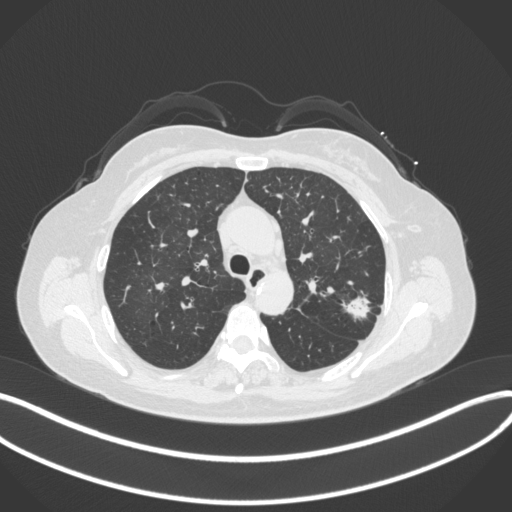
Chest CT, one axial slice. Slice 241 of 330 in the series (ordered by position). 120 kVp. Lung window (W 1500 / L -600 HU). 512 × 512 image matrix, field of view 400 × 400 mm. Patient: female, 60 years. From the clinical record (not read from this slice): clinical TNM (as recorded): T1c N0 M0.
Structures marked on this image (rectangle marked by the reading radiologist):
- lung tumour (recorded histology: adenocarcinoma): bounding box [x1, y1, x2, y2] px = [343, 286, 373, 322]